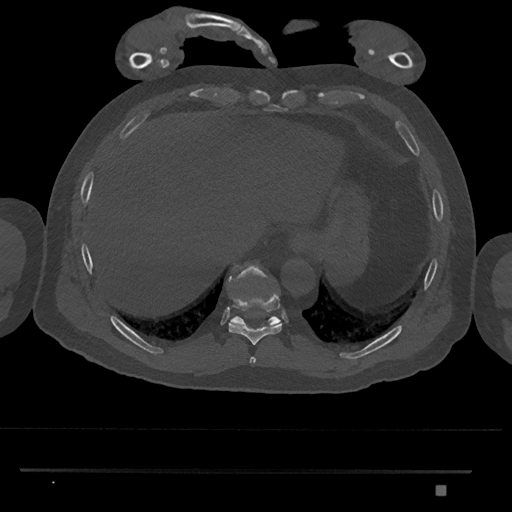
CT including the spine, one axial slice; reconstruction kernel Br40s/3; 120 kVp; bone window (W 1800 / L 400 HU); 0.5 mm slice thickness; 512 × 512 image matrix, field of view 429 × 429 mm. Patient: male, 65 years. Case-level facts recorded for this patient, not image findings: primary cancer: prostate.
Structures marked on this image (semi-automatic segmentation, software-assisted and operator-edited):
- T10 vertebra: bounding box (x1, y1, x2, y2) in pixels: (227, 264, 282, 327)
- T8 vertebra: (250, 357, 256, 364)
- T9 vertebra: (228, 294, 282, 345)